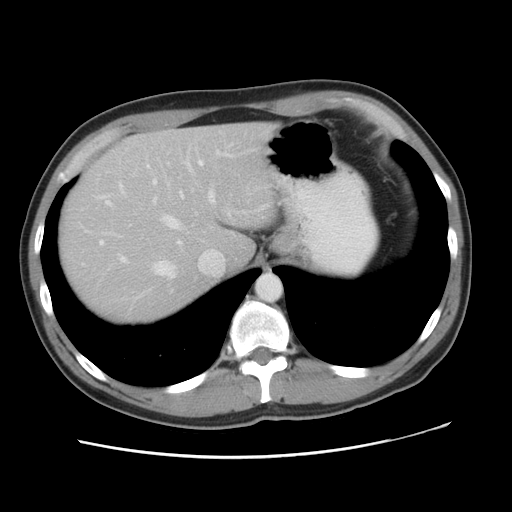
Contrast-enhanced abdominal CT, one axial slice; position 38 of 49 along the scan axis; reconstruction kernel STANDARD; intravenous contrast given; soft-tissue window (W 400 / L 40 HU); 5 mm slice thickness; 512 × 512 image matrix, field of view 363 × 363 mm. Male patient, age 41 years. Case-level facts recorded for this patient, not image findings: diagnosis: colorectal cancer liver metastases, imaged before liver resection; multiple liver metastases: yes; largest metastasis: 0.7 cm; chemotherapy before resection: yes.
Outlined on this slice (expert manual segmentation):
- hepatic veins: bounding box (x1, y1, x2, y2) in pixels: (98, 189, 251, 278)
- liver: (58, 124, 277, 325)
- planned liver remnant (the part of the liver to remain after resection): (102, 124, 277, 270)
- portal vein (with intrahepatic branches): (99, 151, 218, 262)